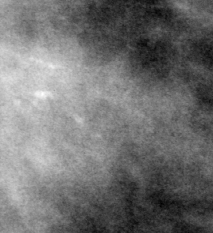
Cropped region of a digitized screen-film mammogram centred on a radiologist-marked abnormality; left breast; MLO view.
Marked abnormality: calcifications, morphology amorphous / pleomorphic, distribution clustered; BI-RADS assessment category 4; pathology (as recorded): malignant.